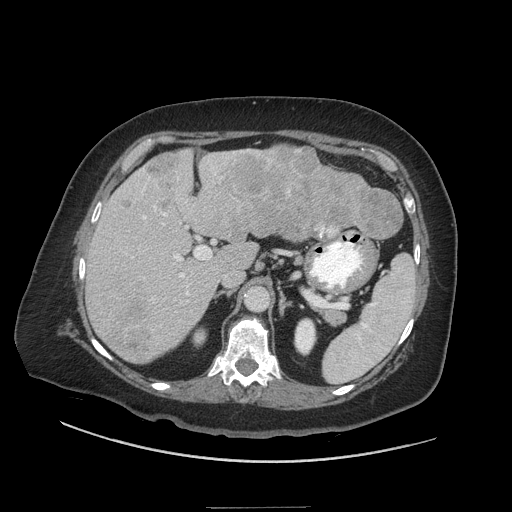
Contrast-enhanced abdominal CT (liver protocol), one axial slice; slice 26 of 81 in the series (ordered by position); reconstruction kernel STANDARD; 140 kVp; soft-tissue window (W 400 / L 40 HU); 2.5 mm slice thickness; 512 × 512 image matrix. From the clinical record (not read from this slice): diagnosis: hepatocellular carcinoma (patient treated with transarterial chemoembolisation; whether this scan precedes or follows treatment is not stated here); TNM stage (as recorded): Stage-II; Child-Pugh class: A; tumour nodularity: multinodular; tumour size: 1.7 cm.
Structures marked on this image (semi-automatic segmentation, software-assisted and operator-edited):
- liver parenchyma outside the tumour (the mass and vessels are separate outlines, so this box may not span the whole liver): bounding box (x1, y1, x2, y2) in pixels: (86, 144, 364, 364)
- mass: (104, 146, 402, 356)
- liver vessels: (124, 149, 250, 304)